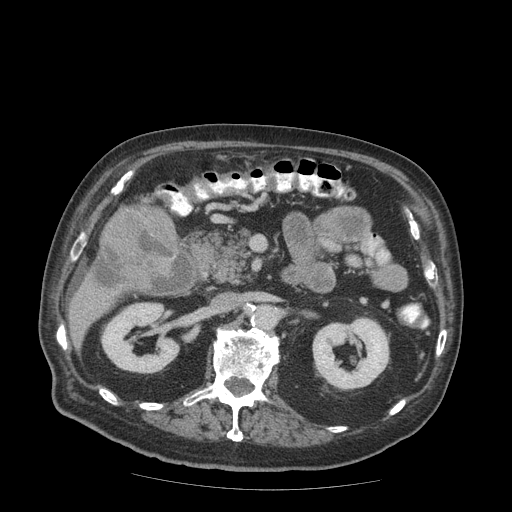
Contrast-enhanced abdominal CT (liver protocol), one axial slice. Position 28 of 99 along the scan axis. 140 kVp. Soft-tissue window (W 400 / L 40 HU). 2.5 mm slice thickness. 512 × 512 image matrix. From the clinical record (not read from this slice): diagnosis: hepatocellular carcinoma (patient treated with transarterial chemoembolisation; whether this scan precedes or follows treatment is not stated here); TNM stage (as recorded): Stage-IIIB; Child-Pugh class: A; tumour differentiation: well differentiated; tumour nodularity: multinodular.
Structures marked on this image (semi-automatically segmented with operator editing):
- liver parenchyma outside the tumour (the mass and vessels are separate outlines, so this box may not span the whole liver): bounding box (x1, y1, x2, y2) in pixels: (68, 200, 180, 348)
- mass: (93, 204, 179, 291)